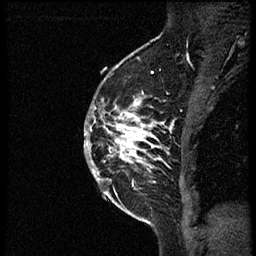
Breast MRI (dynamic contrast-enhanced), one sagittal slice; slice 41 of 56 in the series (ordered by position); dynamic contrast-enhanced study with each time point stored as its own series, time point 2 of 3 at this slice position (early post-contrast, ordered by acquisition time); 1.5 T; TE 4.2 ms, TR 21.3 ms; 2 mm slice thickness; 256 × 256 image matrix. Patient: female, 41 years. From the clinical record (not read from this slice): setting: breast cancer imaged before/during neoadjuvant chemotherapy; receptor status: HER2-positive.
Annotated regions visible in this slice (semi-automatically segmented with operator editing):
- analysis volume of interest (the breast-tissue region the enhancement analysis was run in; not a lesion): bounding box (x1, y1, x2, y2) in pixels: (90, 73, 174, 205)
- tumour enhancement mask (voxels above the 100 % enhancement threshold inside the analysis volume of interest): (90, 92, 167, 181)